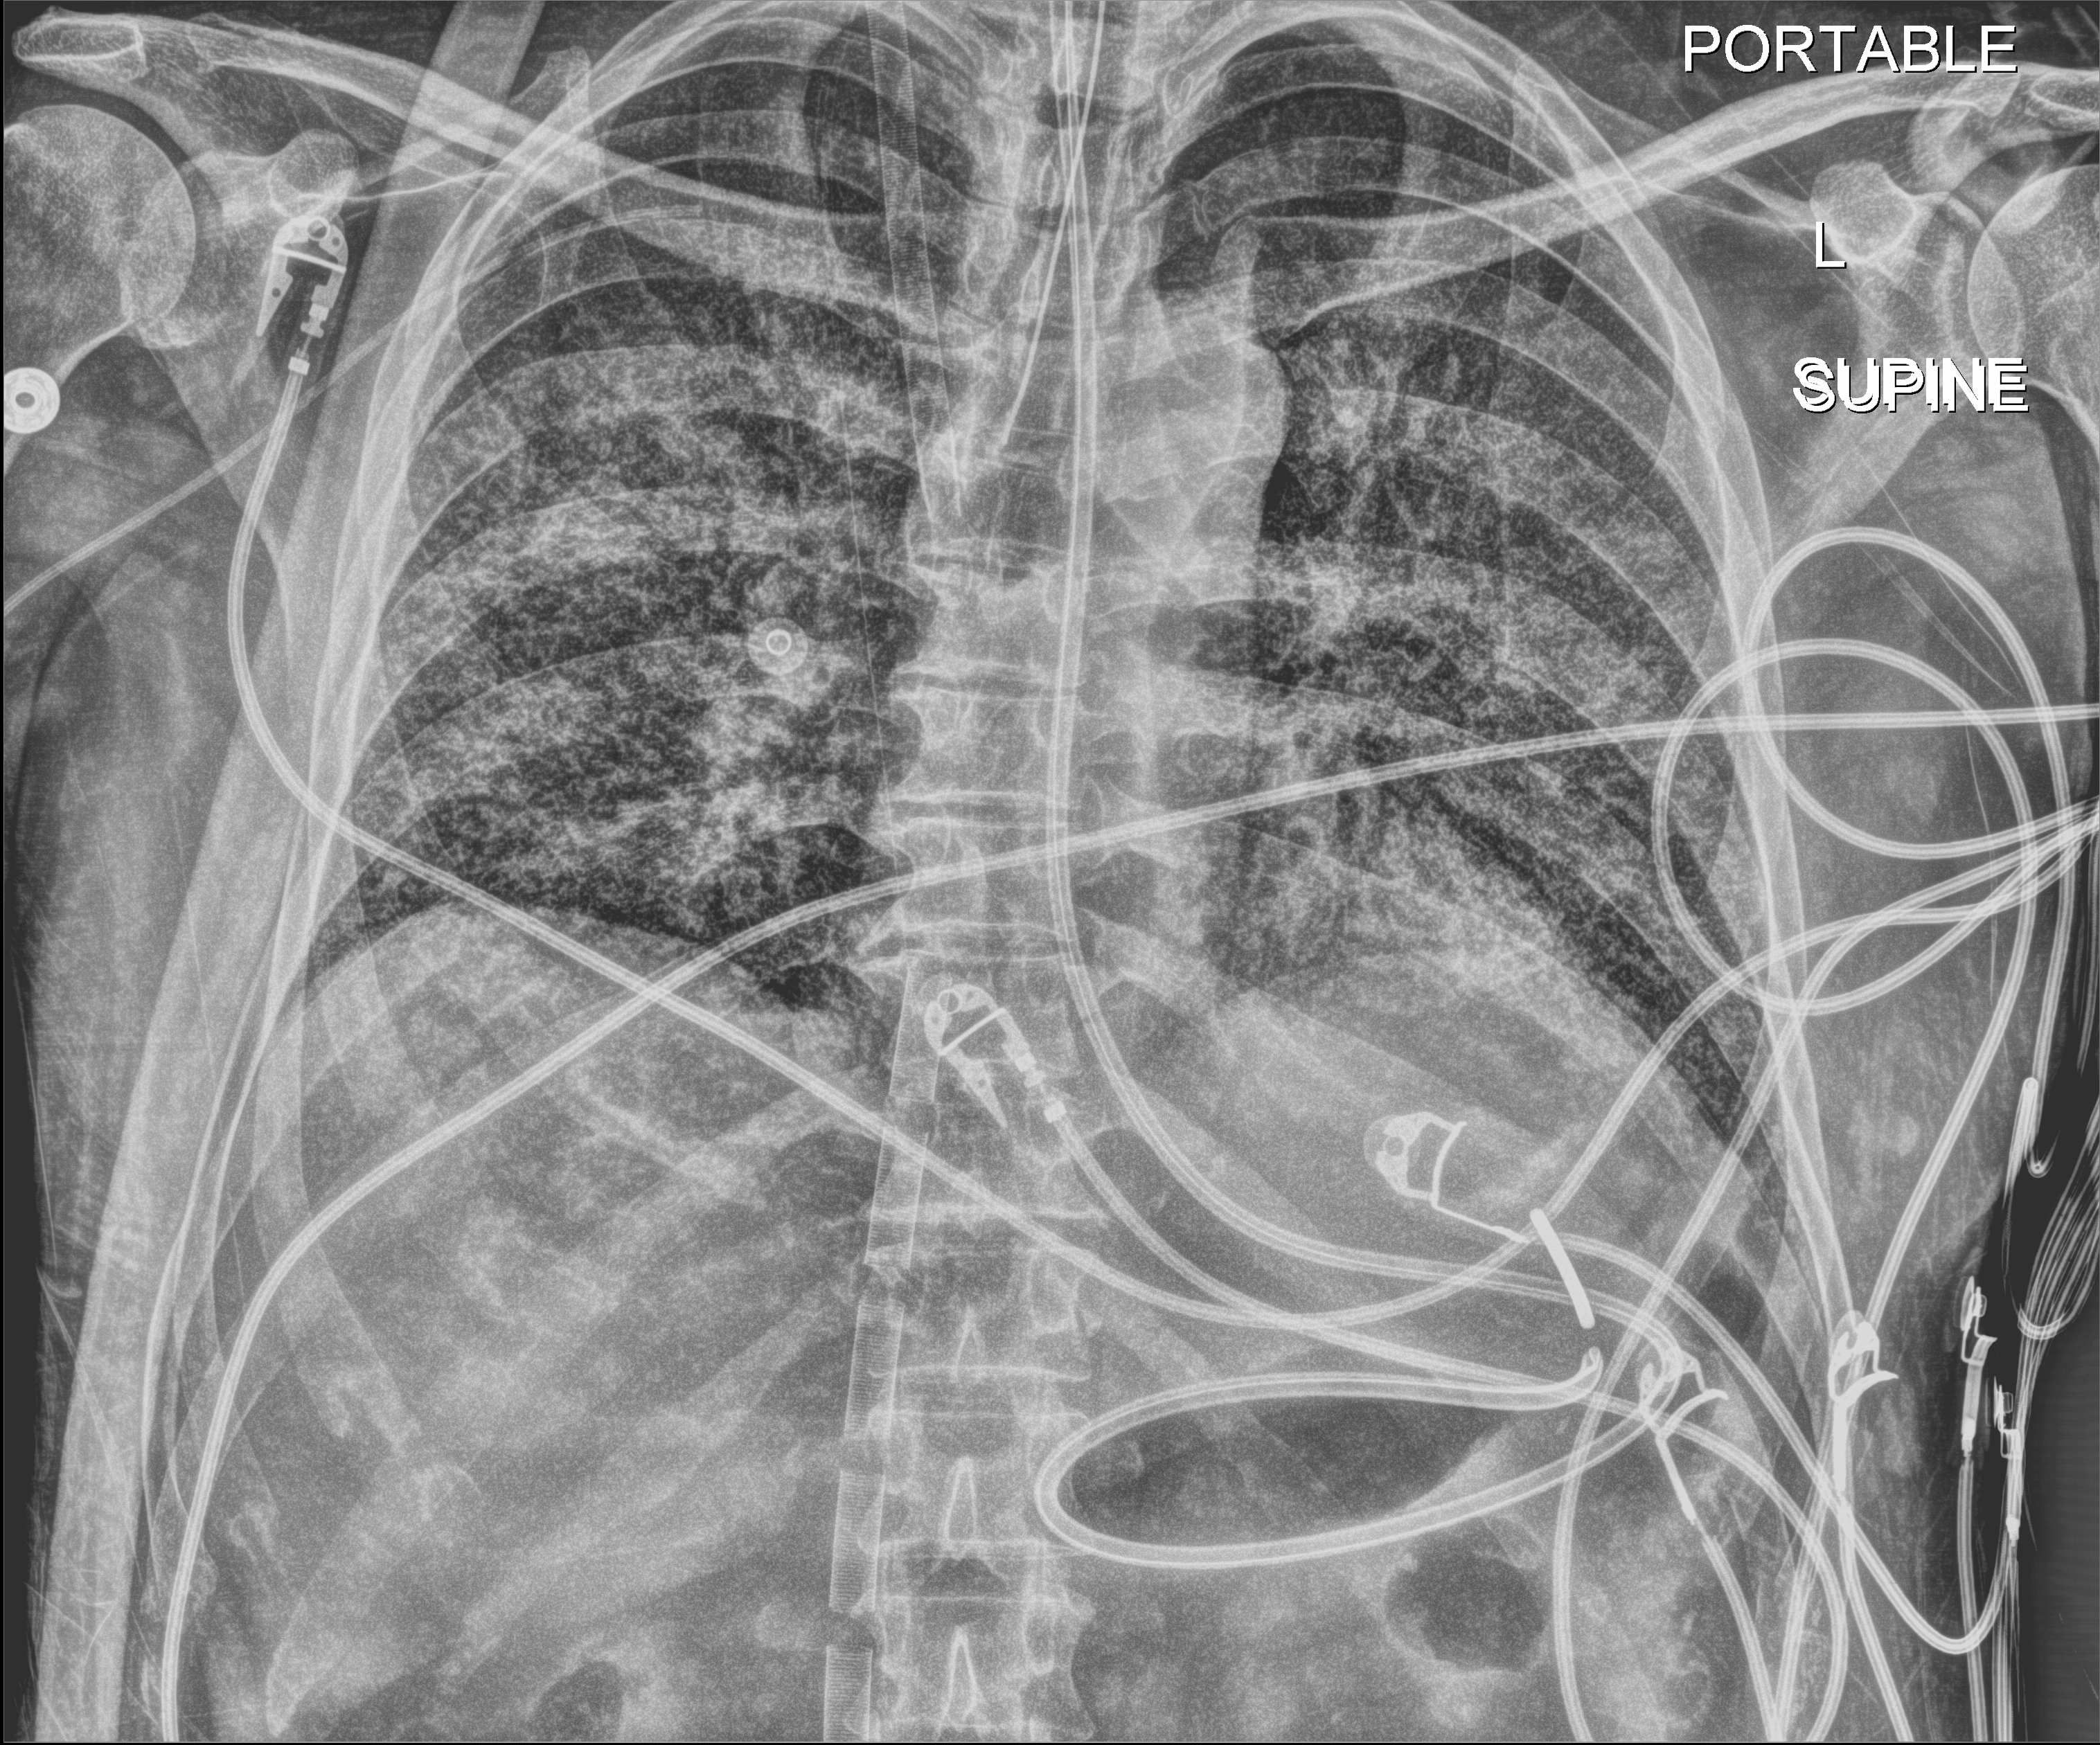
Chest X-ray (portable); anteroposterior (AP) projection. Patient hospitalised with COVID-19; male, aged 18–59 years.
From the hospital-stay record, not from the radiograph (when in the stay this image was taken is not recorded):
- other chronic lung disease (admission record): no
- admitted to intensive care during this hospital stay: yes